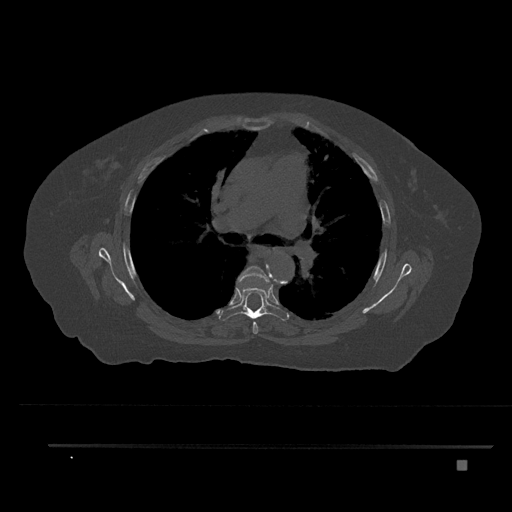
CT including the spine, one axial slice. 120 kVp. Bone window (W 1800 / L 400 HU). 0.5 mm slice thickness. 512 × 512 image matrix, field of view 437 × 437 mm. Female patient, age 76 years. From the clinical record (not read from this slice): primary cancer: lung; vertebrae with lytic lesions (as recorded): T11, L3.
Outlined on this slice (semi-automatically segmented with operator editing):
- T5 vertebra: bounding box <237,266,270,334> (left, top, right, bottom; pixels)
- T6 vertebra: <219,279,289,321>